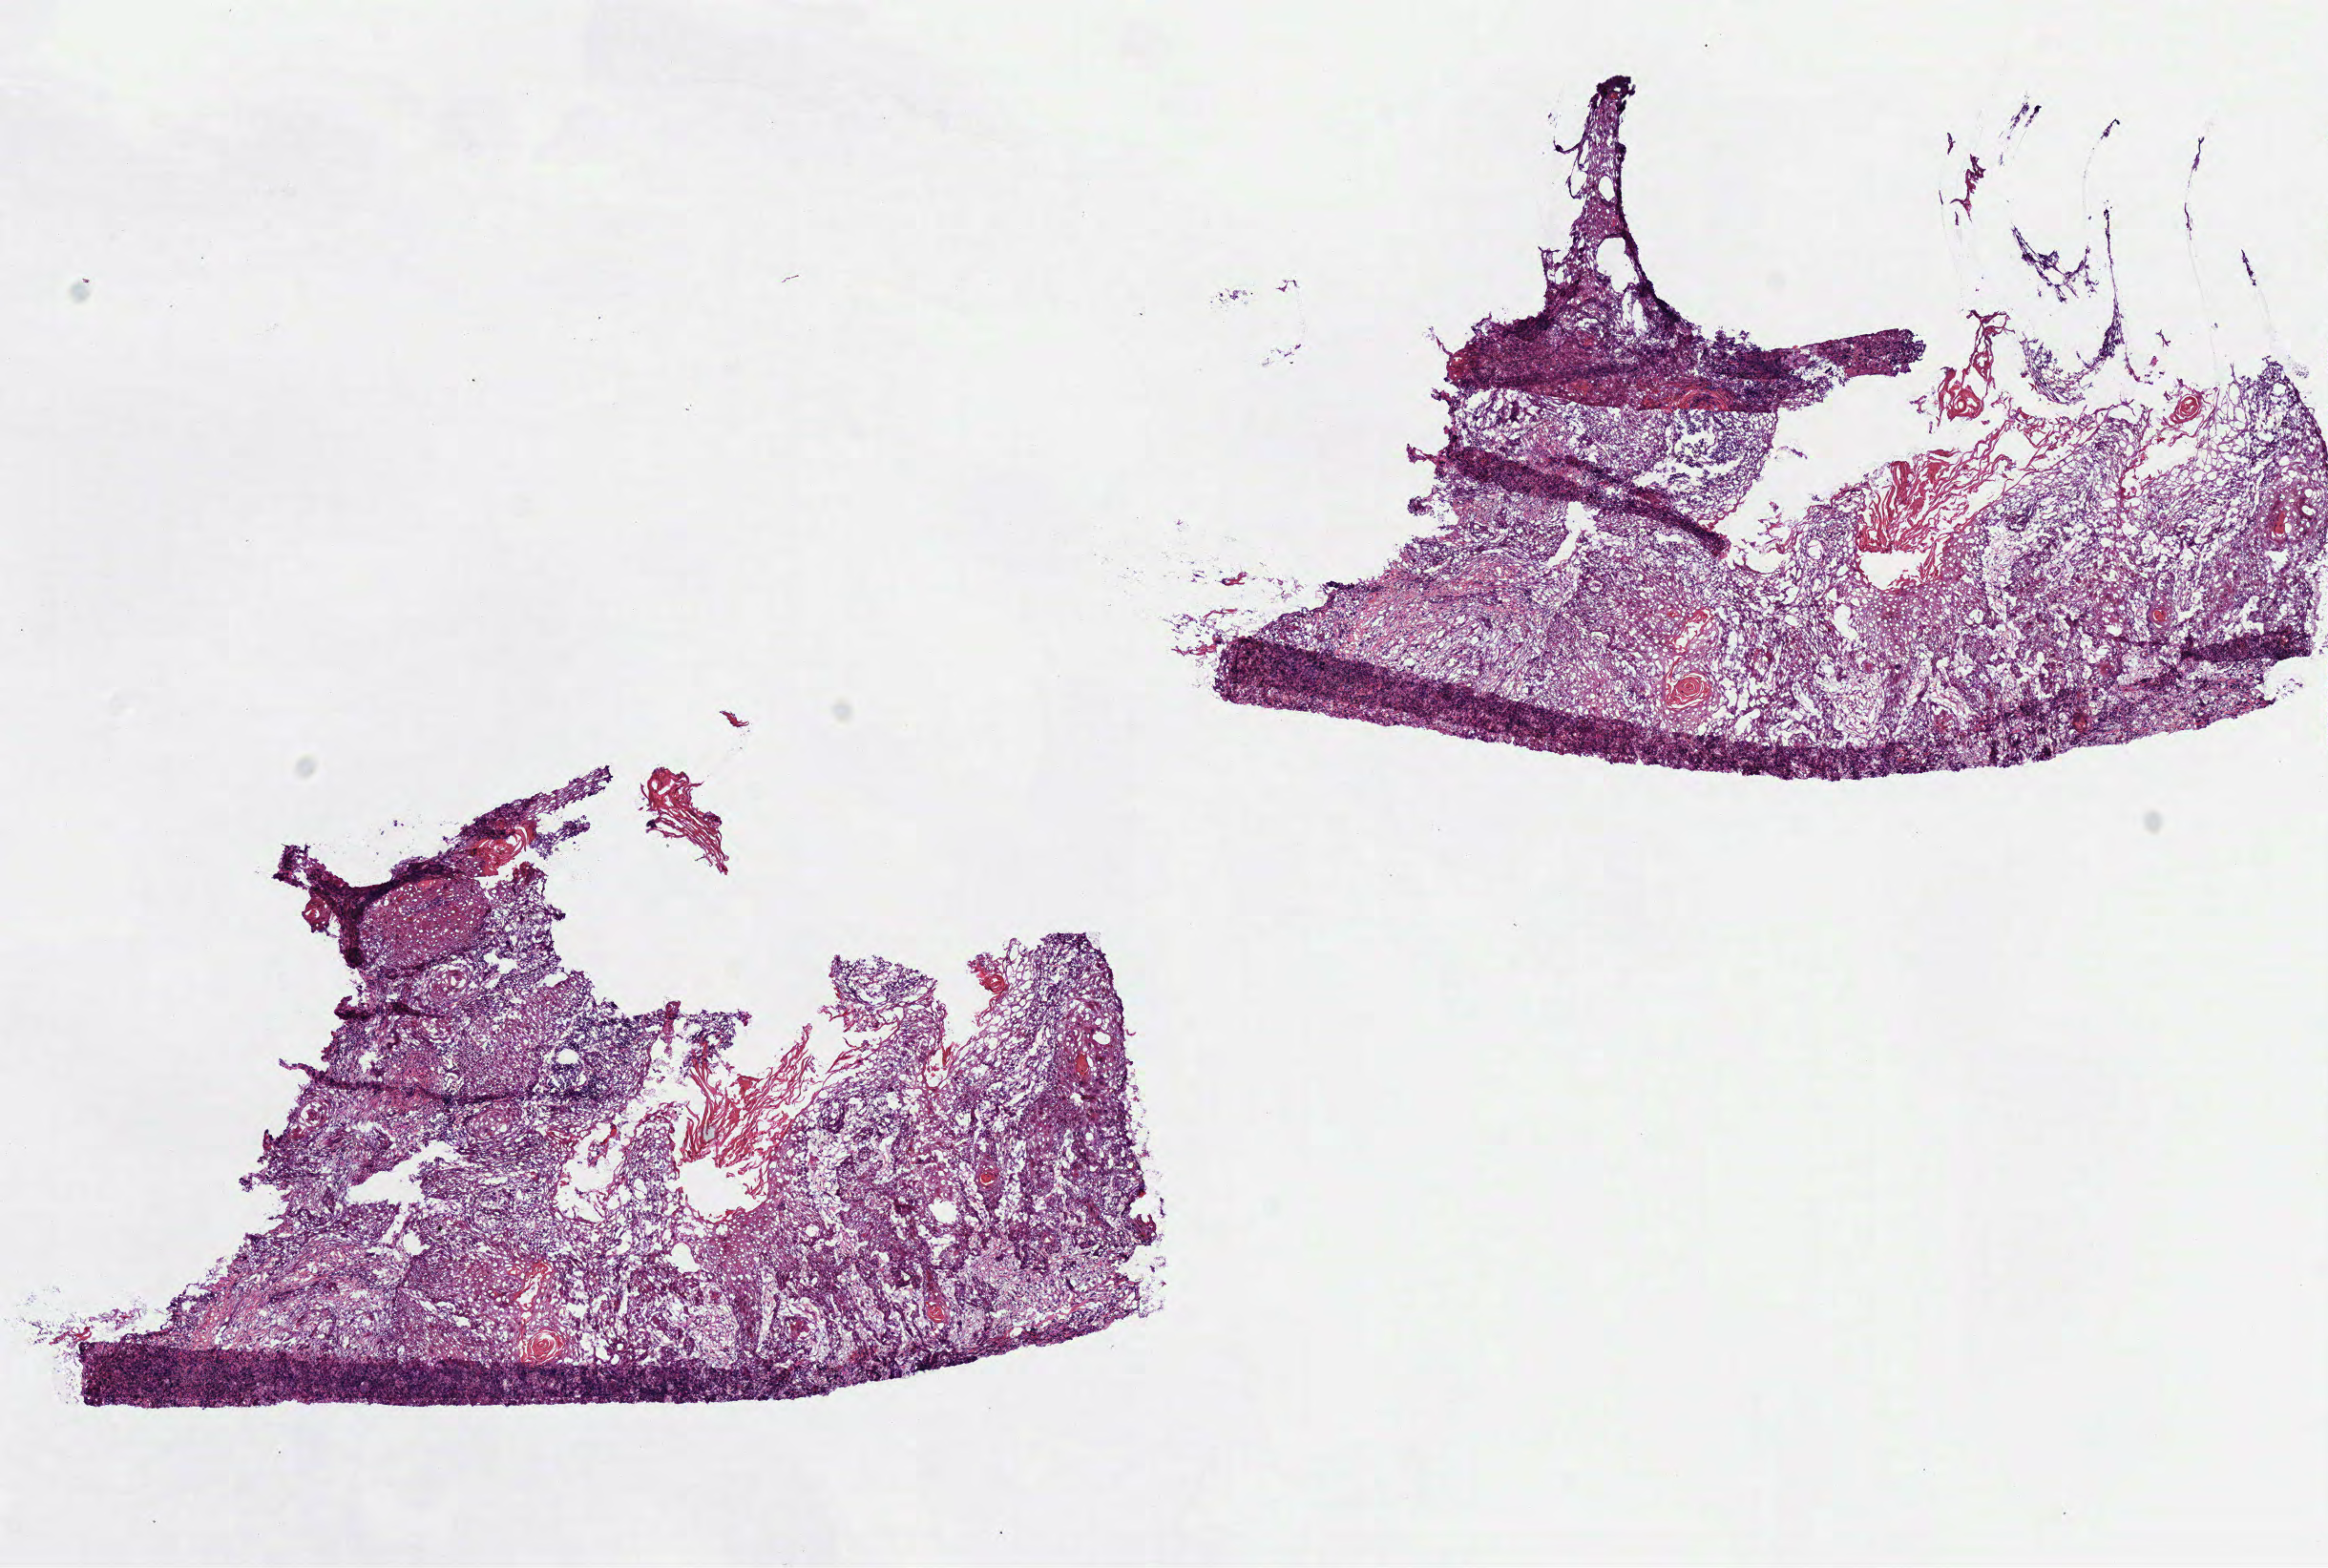
H&E whole-slide image, a low-resolution overview of the entire scanned area, about 9.6 x 6.5 mm, frozen section from the top of the tissue portion, sample: primary tumour, head and neck. Patient: male, age at initial diagnosis 59 years. Histologic grade: G2 (moderately differentiated). Composition of this section per pathologist review: tumour cells 90%, tumour nuclei 80%, normal cells 0%, stromal cells 10%, necrosis 0%.
• diagnosis: Squamous cell carcinoma, NOS (tongue, NOS)
• AJCC pathologic stage: IVA (7th edition)
• TNM: T4a N2b